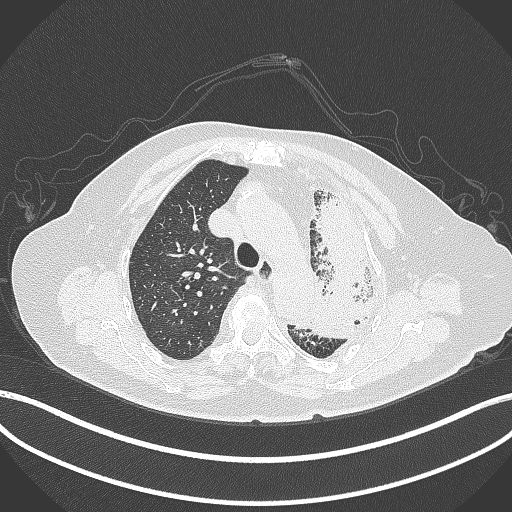
Chest CT, one axial slice; slice 293 of 399 in the series (ordered by position); reconstruction kernel B70f; 120 kVp; lung window (W 1500 / L -600 HU); 1 mm slice thickness; 512 × 512 image matrix, field of view 400 × 400 mm. Patient: female, 75 years. From the clinical record (not read from this slice): clinical TNM (as recorded): T3 N3 M1.
Structures marked on this image (bounding box drawn by a radiologist):
- lung tumour (recorded histology: adenocarcinoma): bounding box (x1, y1, x2, y2) in pixels: (298, 185, 390, 341)